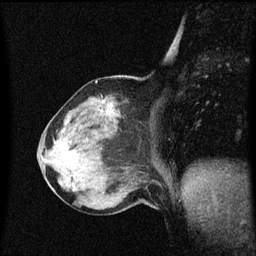
Breast MRI (dynamic contrast-enhanced), one sagittal slice; slice 23 of 60 in the series (ordered by position); dynamic contrast-enhanced series, image 2 of 3 at this slice position (ordered by acquisition); 1.5 T; TE 4.2 ms, TR 8.4 ms; 256 × 256 image matrix, field of view 200 × 200 mm. Female patient, age 64 years. From the clinical record (not read from this slice): setting: breast cancer imaged before/during neoadjuvant chemotherapy; receptor status: HR-positive, HER2-negative.
Structures marked on this image (semi-automatically segmented with operator editing):
- analysis volume of interest (the breast-tissue region the enhancement analysis was run in; not a lesion): bounding box (x1, y1, x2, y2) in pixels: (58, 98, 123, 167)
- tumour enhancement mask (voxels above the 70 % enhancement threshold inside the analysis volume of interest): (104, 100, 113, 115)